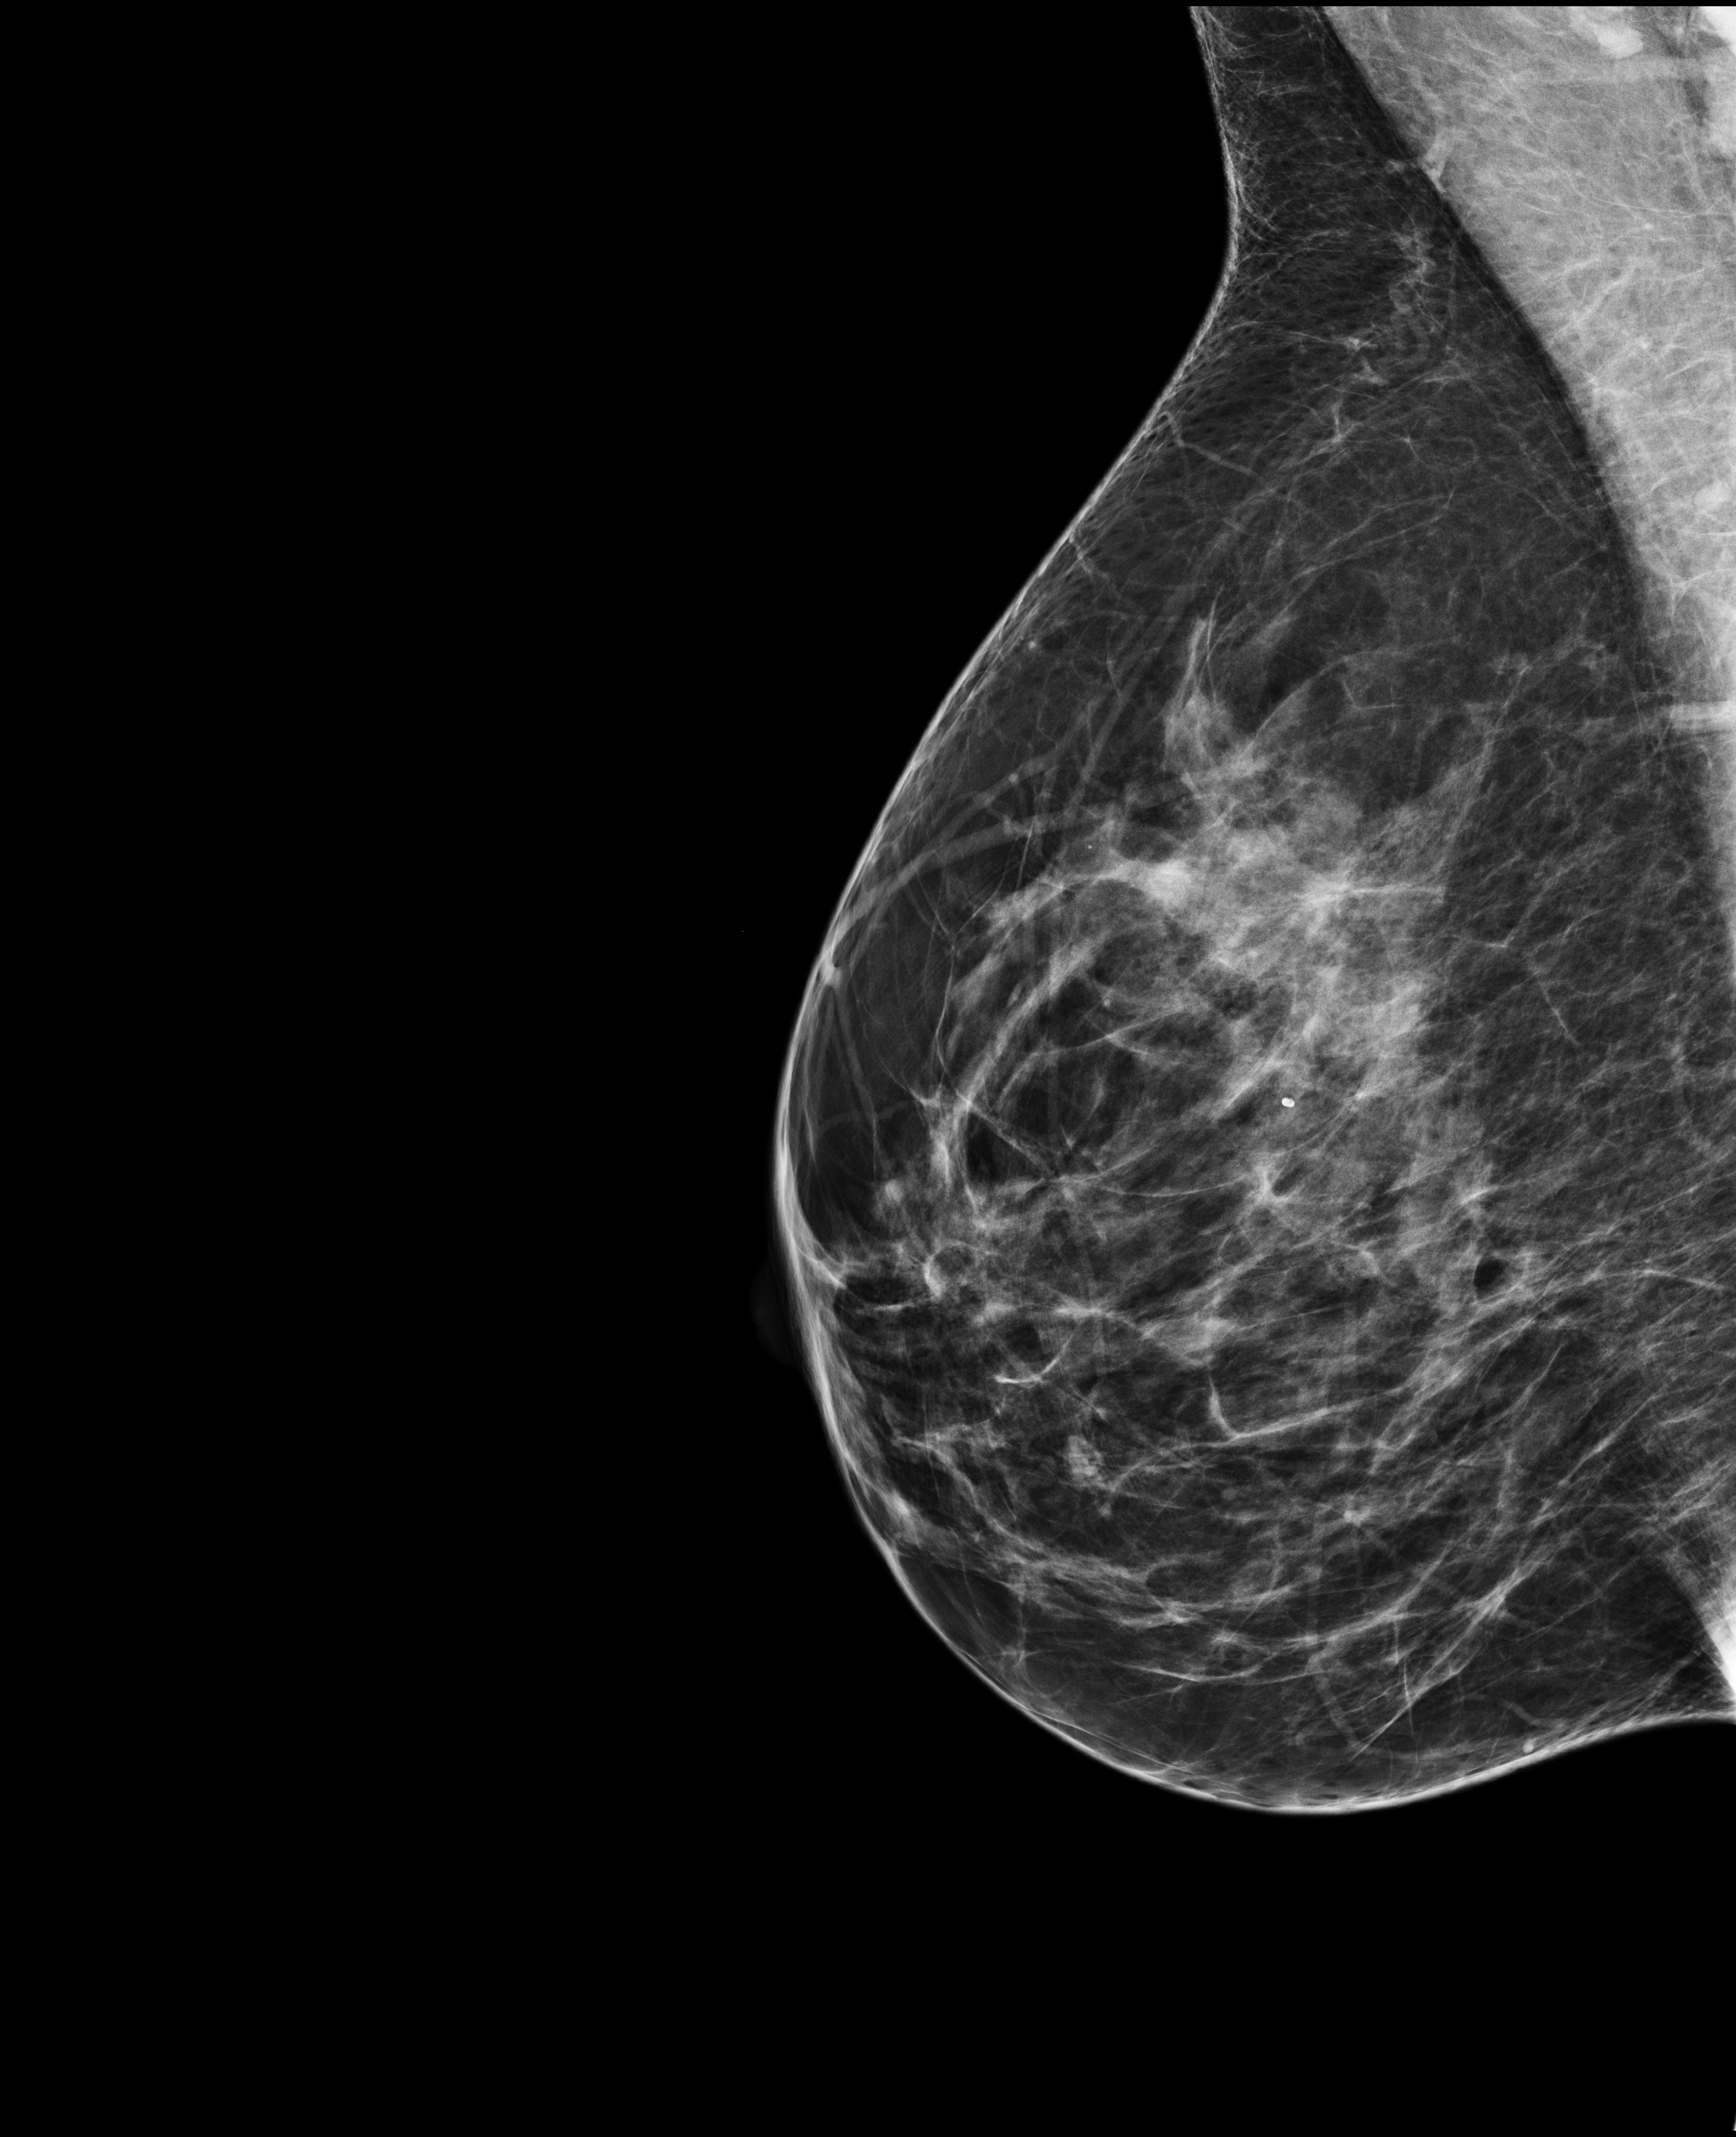
Digital mammogram (FFDM), right breast, medio-lateral oblique projection, annual screening mammography examination, compressed breast thickness 70 mm, system: Selenia Dimensions. Female patient, age 47 years.
- breast density at the screening exam (both breasts): heterogeneously dense (BI-RADS density category c)
- final BI-RADS assessment for this screening round (tomosynthesis exam, both breasts): category 2
- recall: no recall after this screen